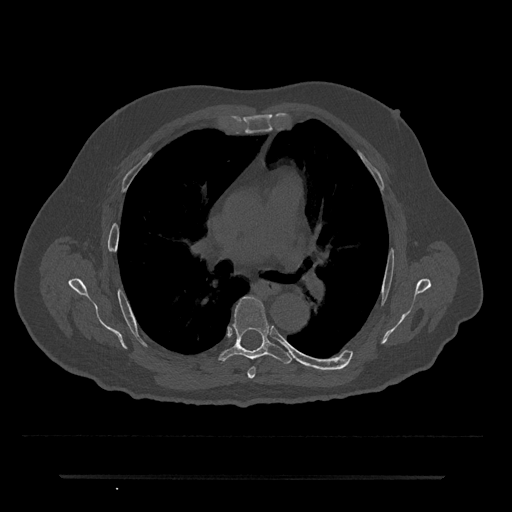
CT including the spine, one axial slice; position 443 of 797 along the scan axis; 120 kVp; bone window (W 1800 / L 400 HU); 0.5 mm slice thickness; 512 × 512 image matrix, field of view 437 × 437 mm. Male patient, age 69 years. Case-level facts recorded for this patient, not image findings: primary cancer: prostate.
Structures marked on this image (semi-automatically segmented with operator editing):
- T5 vertebra: bounding box <247,367,256,379> (left, top, right, bottom; pixels)
- T6 vertebra: <218,297,293,364>